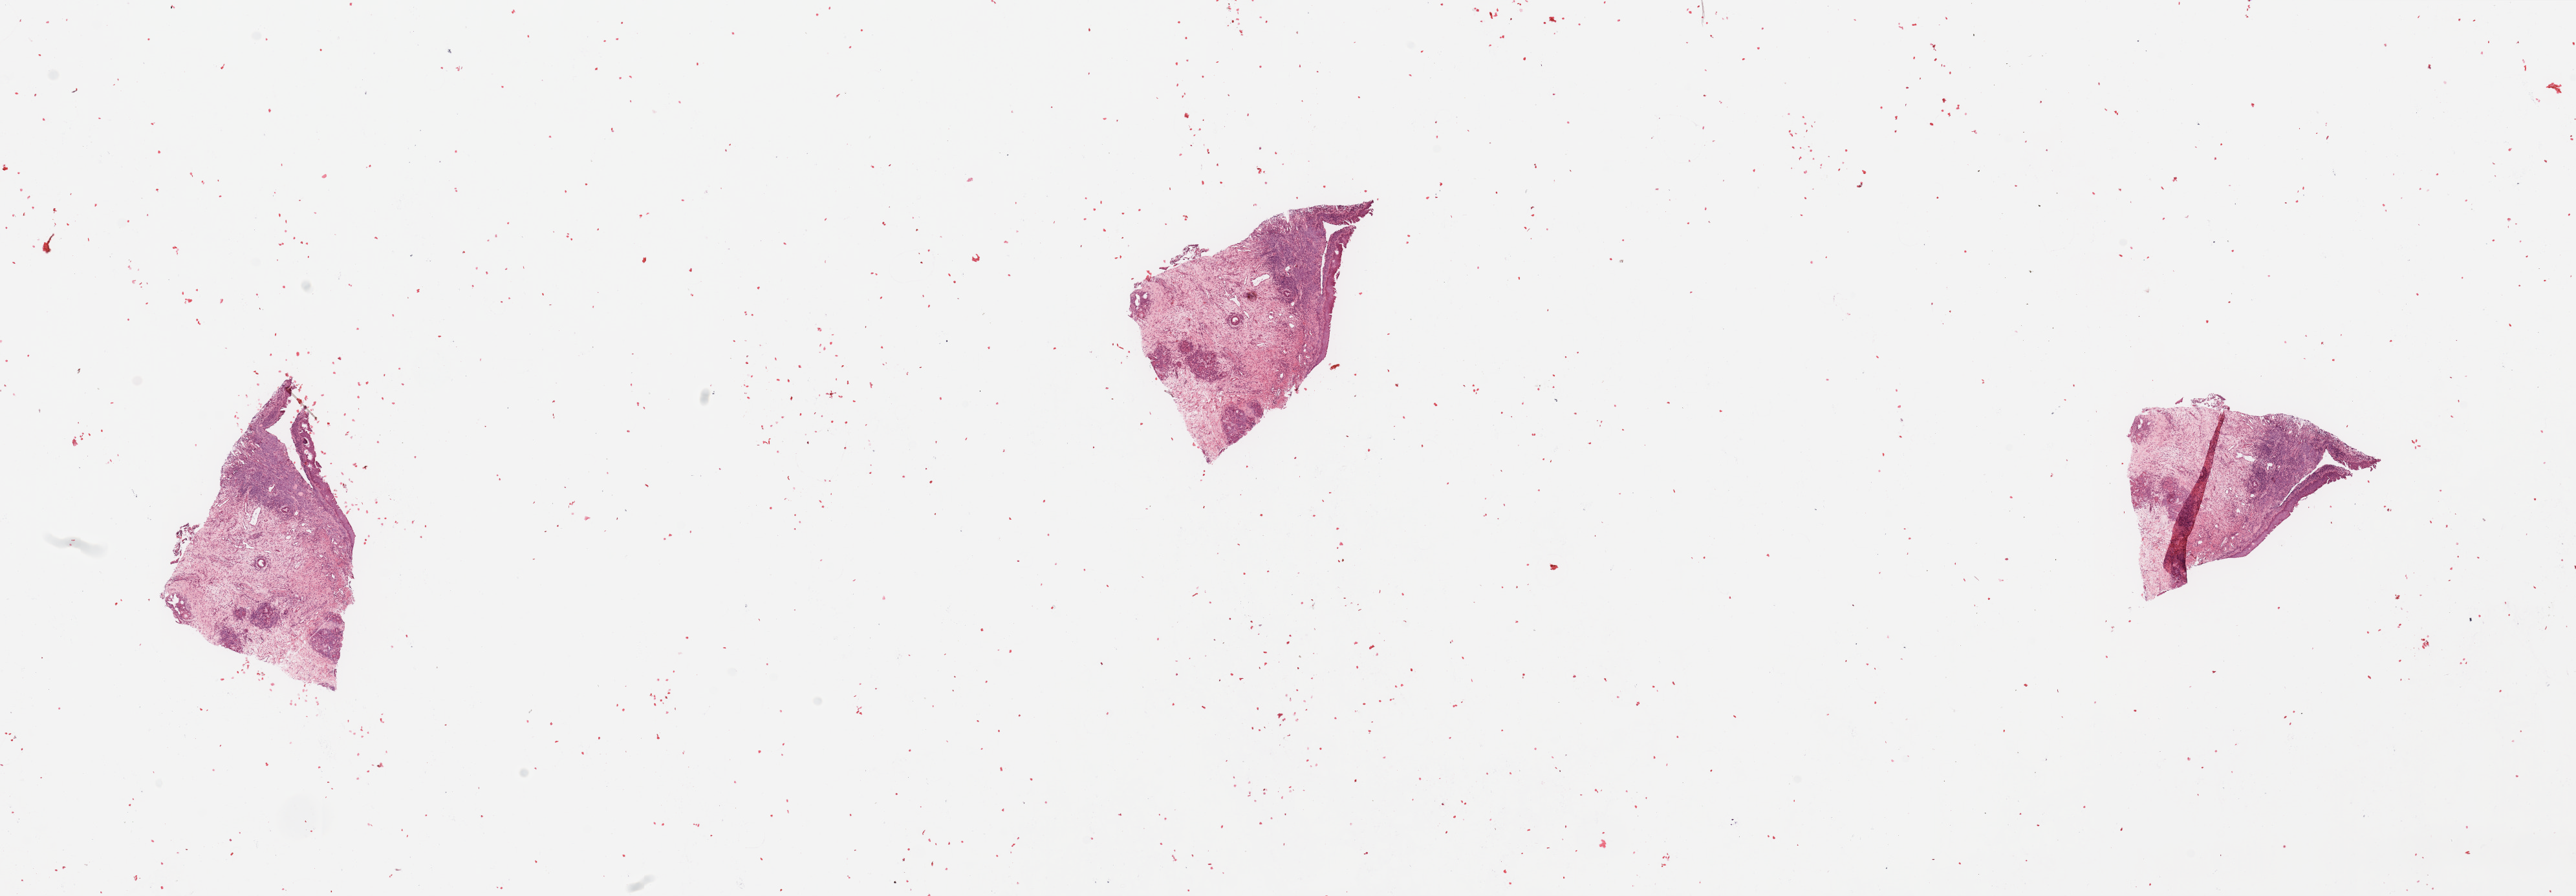
Whole-slide histology image, H&E, shown as a low-resolution overview of the whole scanned area (about 31.5 x 11.0 mm, from a 20x scan); normal (non-tumour) tissue sample, sampled site: larynx. 69-year-old male patient.
This section: normal (non-tumour) tissue from the same patient. Patient diagnosis: Squamous cell carcinoma, NOS (larynx, NOS).